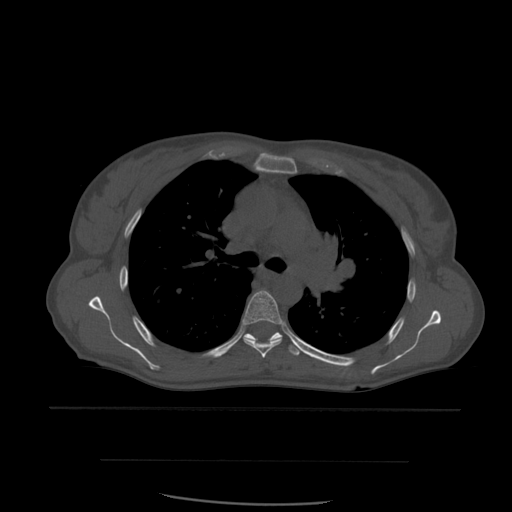
CT including the spine, one axial slice. Position 405 of 574 along the scan axis. Bone window (W 1800 / L 400 HU). 1.25 mm slice thickness. 512 × 512 image matrix, field of view 392 × 392 mm. Patient age 48 years. Case-level facts recorded for this patient, not image findings: primary cancer: lung; vertebrae with lytic lesions (as recorded): T11.
Annotated regions visible in this slice (semi-automatically segmented with operator editing):
- T5 vertebra: bounding box [x1, y1, x2, y2] px = [242, 291, 284, 359]
- T6 vertebra: [246, 332, 300, 357]